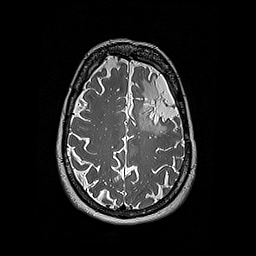
Brain MRI from a brain-tumour surgery series, one axial slice; 1 mm slice thickness; 256 × 256 image matrix, field of view 250 × 250 mm. From the clinical record (not read from this slice): histopathology: Oligodendroglioma; WHO grade: 2; IDH mutation: yes; tumour location: Left Frontal.
Outlined on this slice (manually delineated by an expert):
- tumour: bounding box <134,80,158,132> (left, top, right, bottom; pixels)